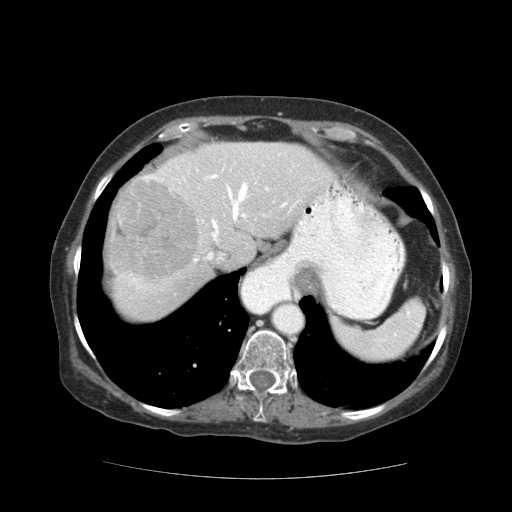
Contrast-enhanced abdominal CT (liver protocol), one axial slice. Position 91 of 111 along the scan axis. Reconstruction kernel STANDARD. Soft-tissue window (W 400 / L 40 HU). 2.5 mm slice thickness. 512 × 512 image matrix, field of view 360 × 360 mm. From the clinical record (not read from this slice): diagnosis: hepatocellular carcinoma (patient treated with transarterial chemoembolisation; whether this scan precedes or follows treatment is not stated here); TNM stage (as recorded): Stage-I; Child-Pugh class: A; tumour differentiation: moderately-poorly differentiated; tumour size: 7.3 cm.
Structures marked on this image (semi-automatically segmented with operator editing):
- abdominal aorta: bounding box (x1, y1, x2, y2) in pixels: (274, 304, 304, 334)
- liver parenchyma outside the tumour (the mass and vessels are separate outlines, so this box may not span the whole liver): (106, 142, 335, 320)
- mass: (110, 181, 199, 284)
- liver vessels: (132, 146, 329, 282)